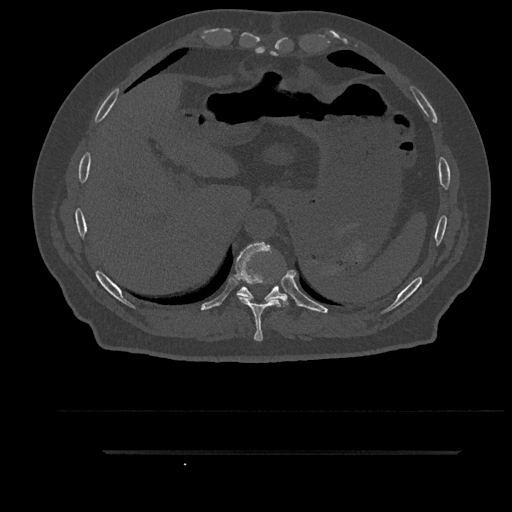
CT including the spine, one axial slice. Slice 397 of 797 in the series (ordered by position). Reconstruction kernel Br40s/3. 120 kVp. Bone window (W 1800 / L 400 HU). 0.5 mm slice thickness. 512 × 512 image matrix, field of view 432 × 432 mm. Patient: male, 63 years. From the clinical record (not read from this slice): primary cancer: renal; vertebrae with lytic lesions (as recorded): T8.
Annotated regions visible in this slice (semi-automatic segmentation, software-assisted and operator-edited):
- T10 vertebra: bounding box [x1, y1, x2, y2] px = [236, 286, 288, 303]
- T9 vertebra: [235, 242, 289, 341]